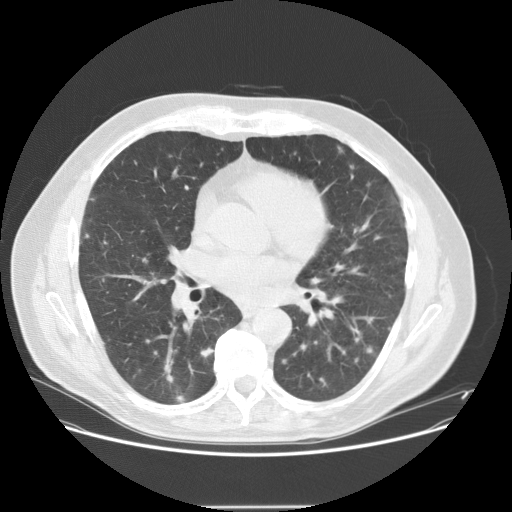
Low-dose screening chest CT, one axial slice. 120 kVp. Lung window (W 1500 / L -600 HU). 2.5 mm slice thickness. 512 × 512 image matrix, field of view 400 × 400 mm.
Outlined on this slice (manually delineated by an expert):
- lesion 7 (tumor): box from (x=366, y=346) to (x=373, y=354) px